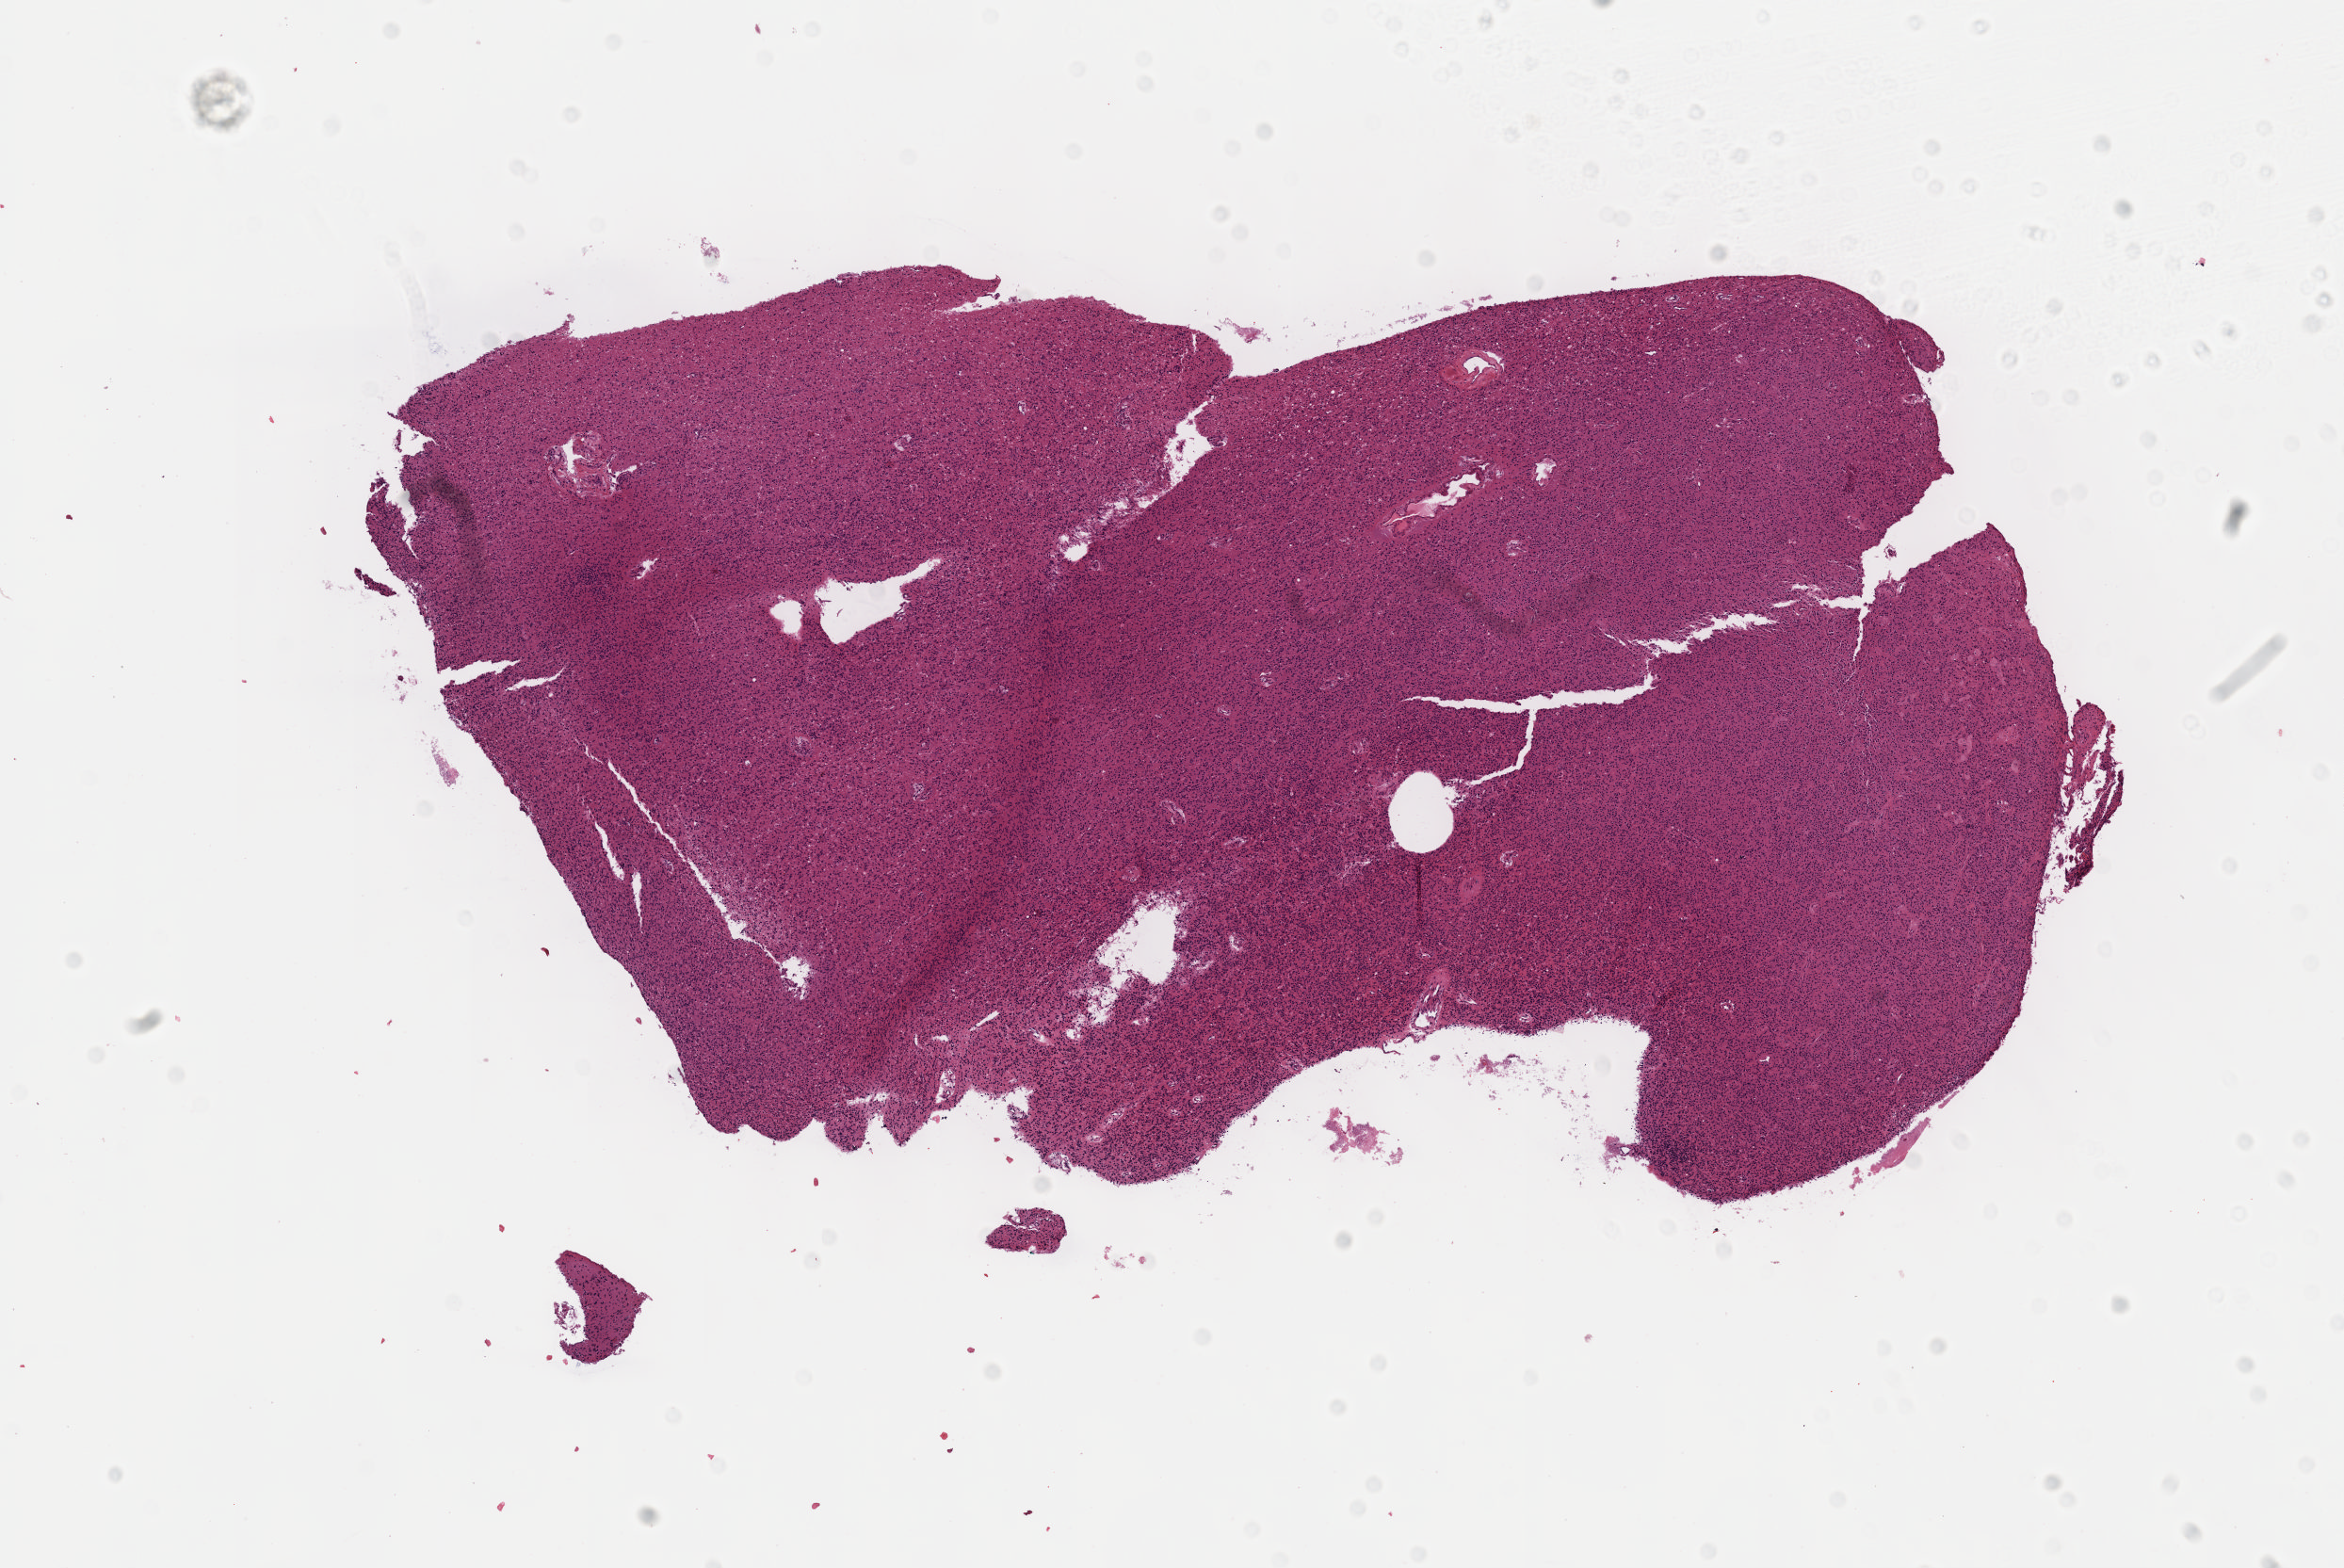
Hematoxylin and eosin (H&E) stained whole-slide image, whole scanned area (about 10.1 x 6.7 mm, from a 40x scan) shown as a low-resolution overview, FFPE section, sample: primary tumour, brain. Patient: male, age at initial diagnosis 39 years. Histologic grade: G2 (moderately differentiated).
• laterality: right
• pathologic diagnosis: Oligodendroglioma, NOS